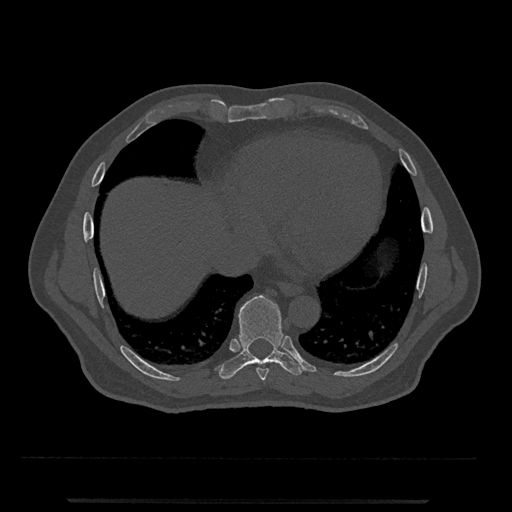
CT including the spine, one axial slice. Slice 589 of 797 in the series (ordered by position). Reconstruction kernel Br40s/3. Bone window (W 1800 / L 400 HU). 512 × 512 image matrix. Male patient, age 63 years. Case-level facts recorded for this patient, not image findings: primary cancer: prostate.
Outlined on this slice (semi-automatically segmented with operator editing):
- T8 vertebra: bounding box <256,367,269,381> (left, top, right, bottom; pixels)
- T9 vertebra: <219,295,304,379>